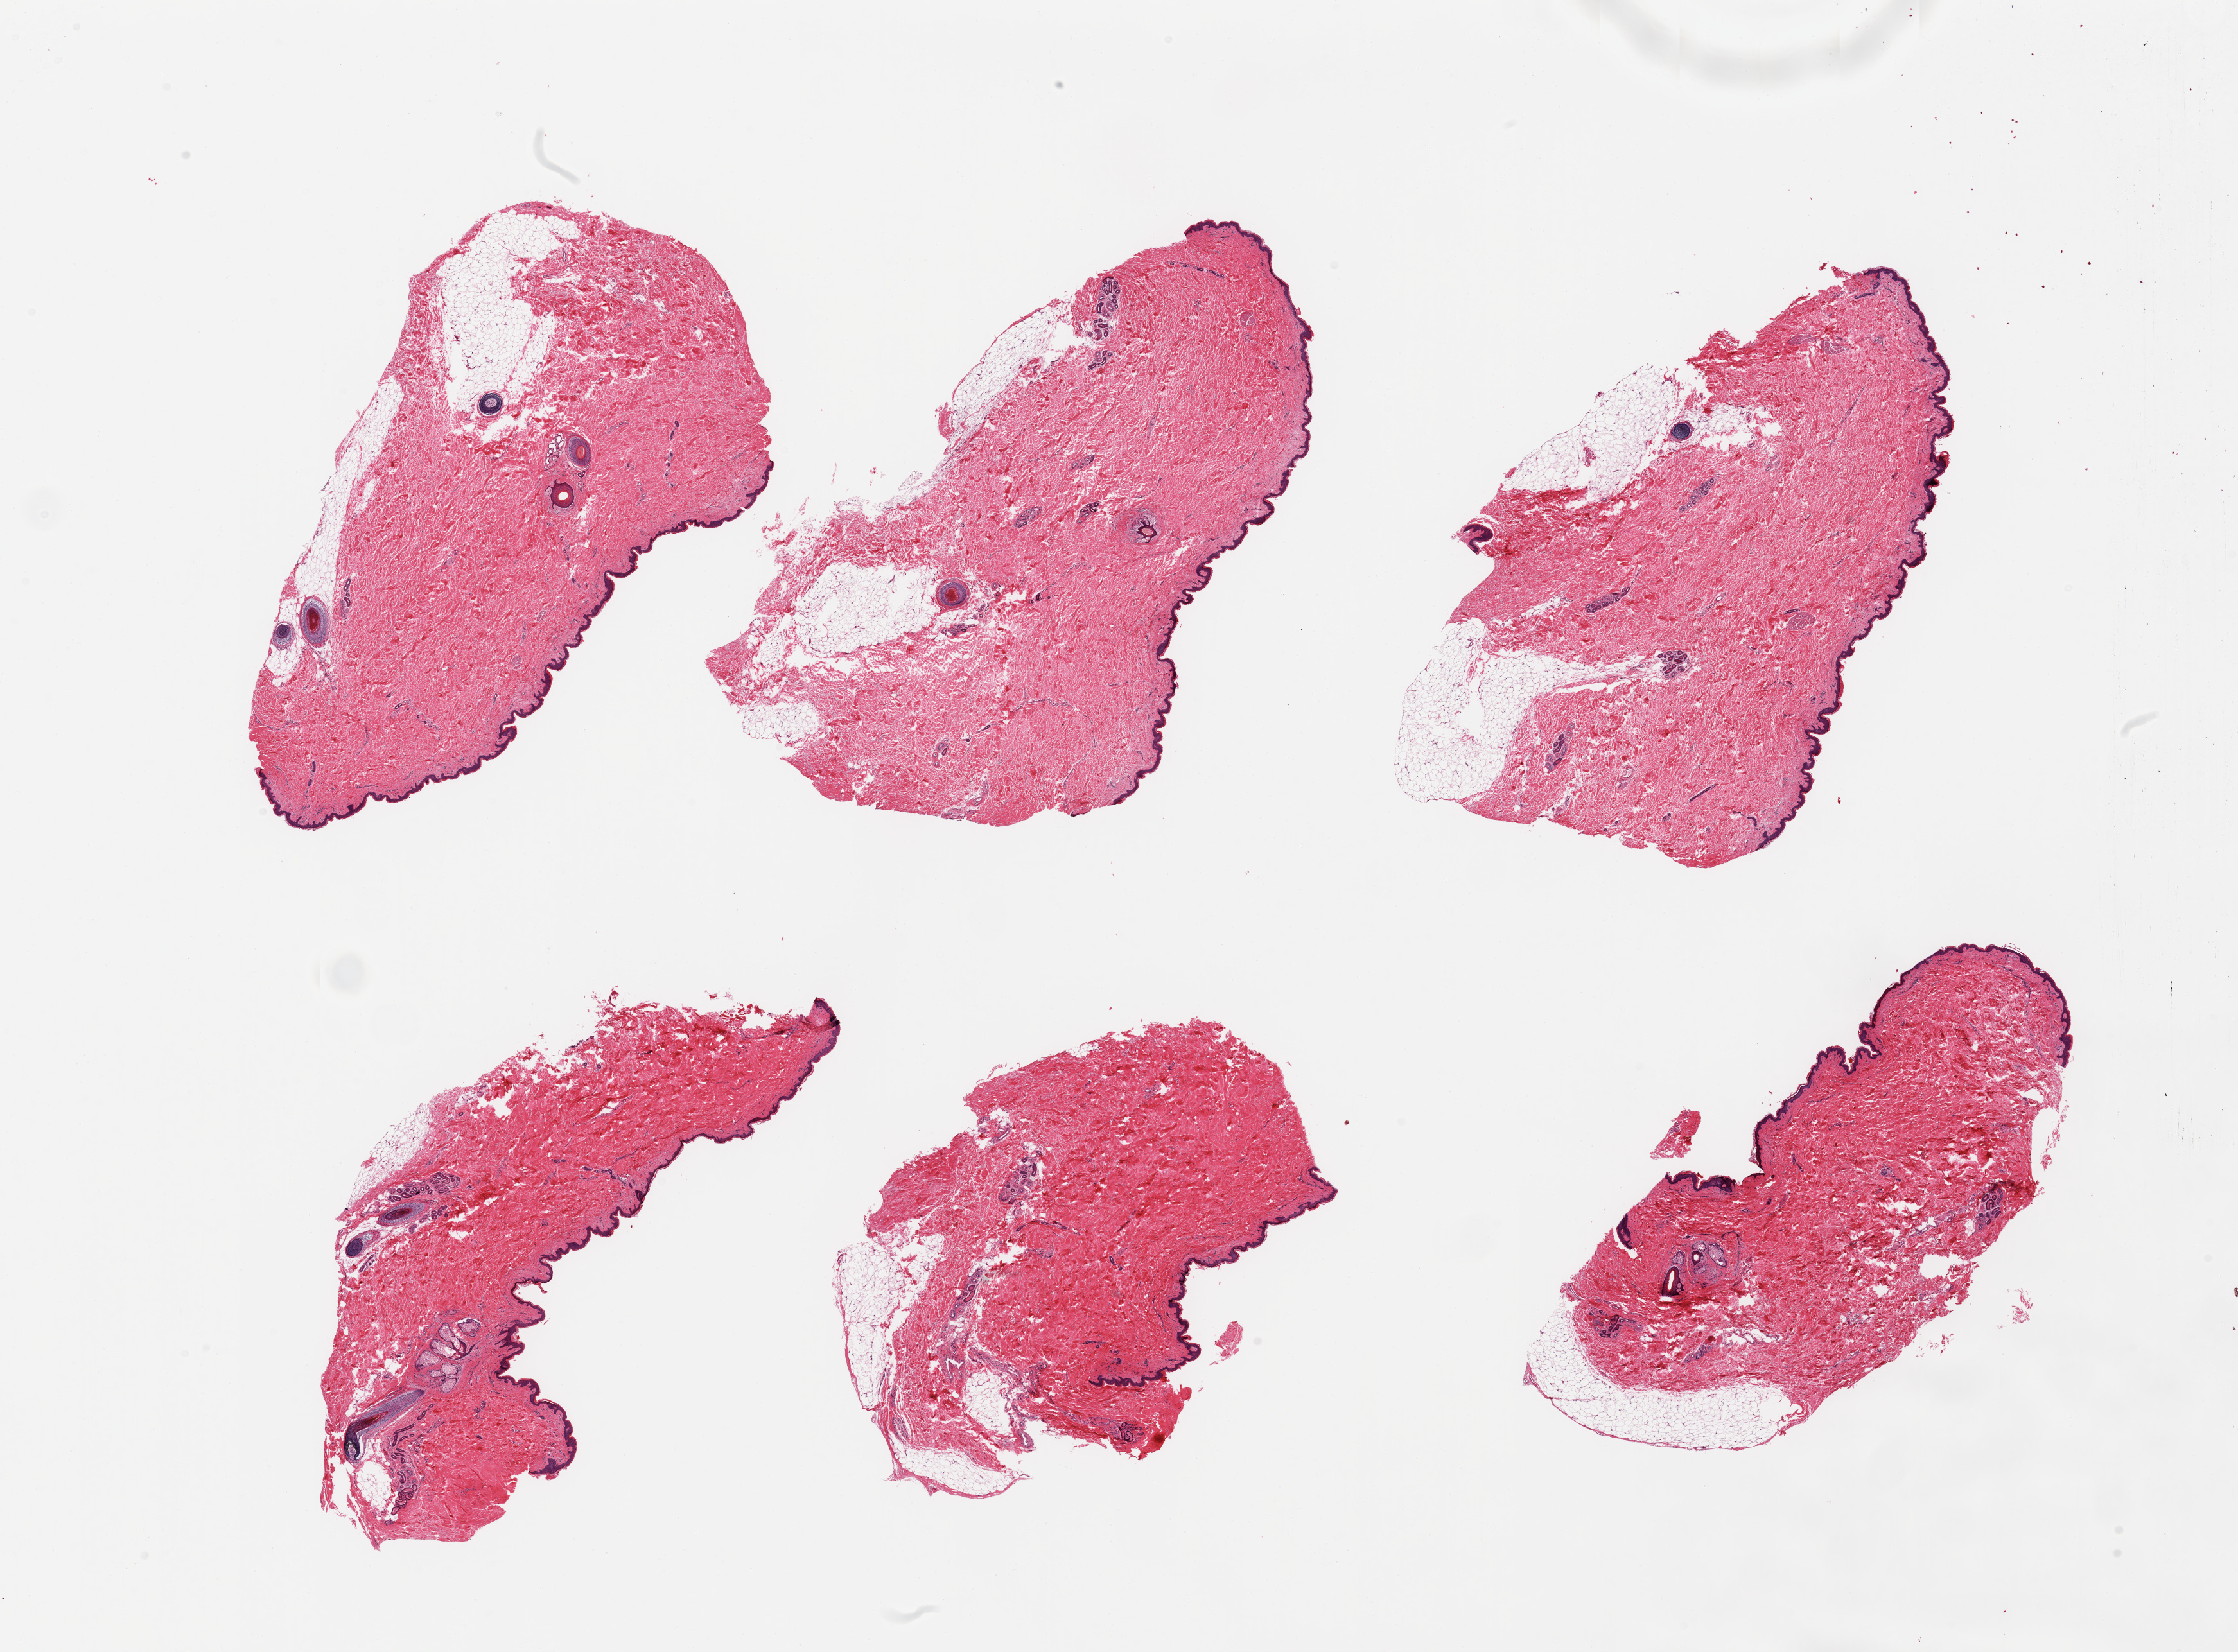
Whole-slide image, hematoxylin and eosin (H&E) stain, brightfield — low-resolution overview of the scanned area, about 27.6 x 20.4 mm; PAXgene-fixed paraffin-embedded (PFPE) section; sampled site (target tissue): skin of suprapubic region; tissue donor sample. Male donor.
Reviewer comment on this tissue sample: 2 pieces, trace adherent and minimal intra-dermal fat; Squamous epithelium is ~30-40 microns.